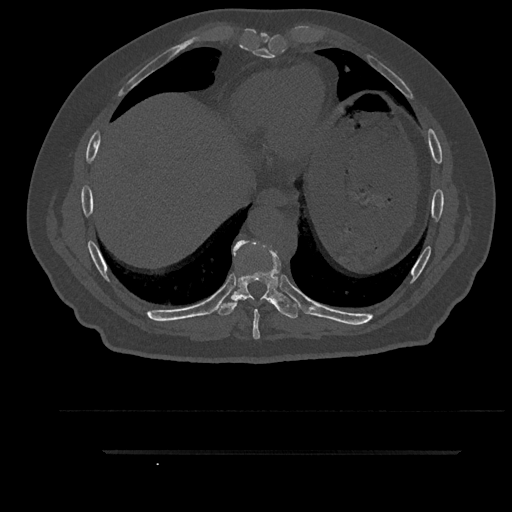
CT including the spine, one axial slice. Position 443 of 797 along the scan axis. Reconstruction kernel Br40s/3. 120 kVp. Bone window (W 1800 / L 400 HU). 0.5 mm slice thickness. 512 × 512 image matrix, field of view 432 × 432 mm. Patient: male, 63 years. Case-level facts recorded for this patient, not image findings: primary cancer: renal; vertebrae with lytic lesions (as recorded): T8.
Structures marked on this image (semi-automatically segmented with operator editing):
- T8 vertebra: box from (x=234, y=240) to (x=274, y=339) px
- T9 vertebra: (x=214, y=241)–(x=298, y=319)